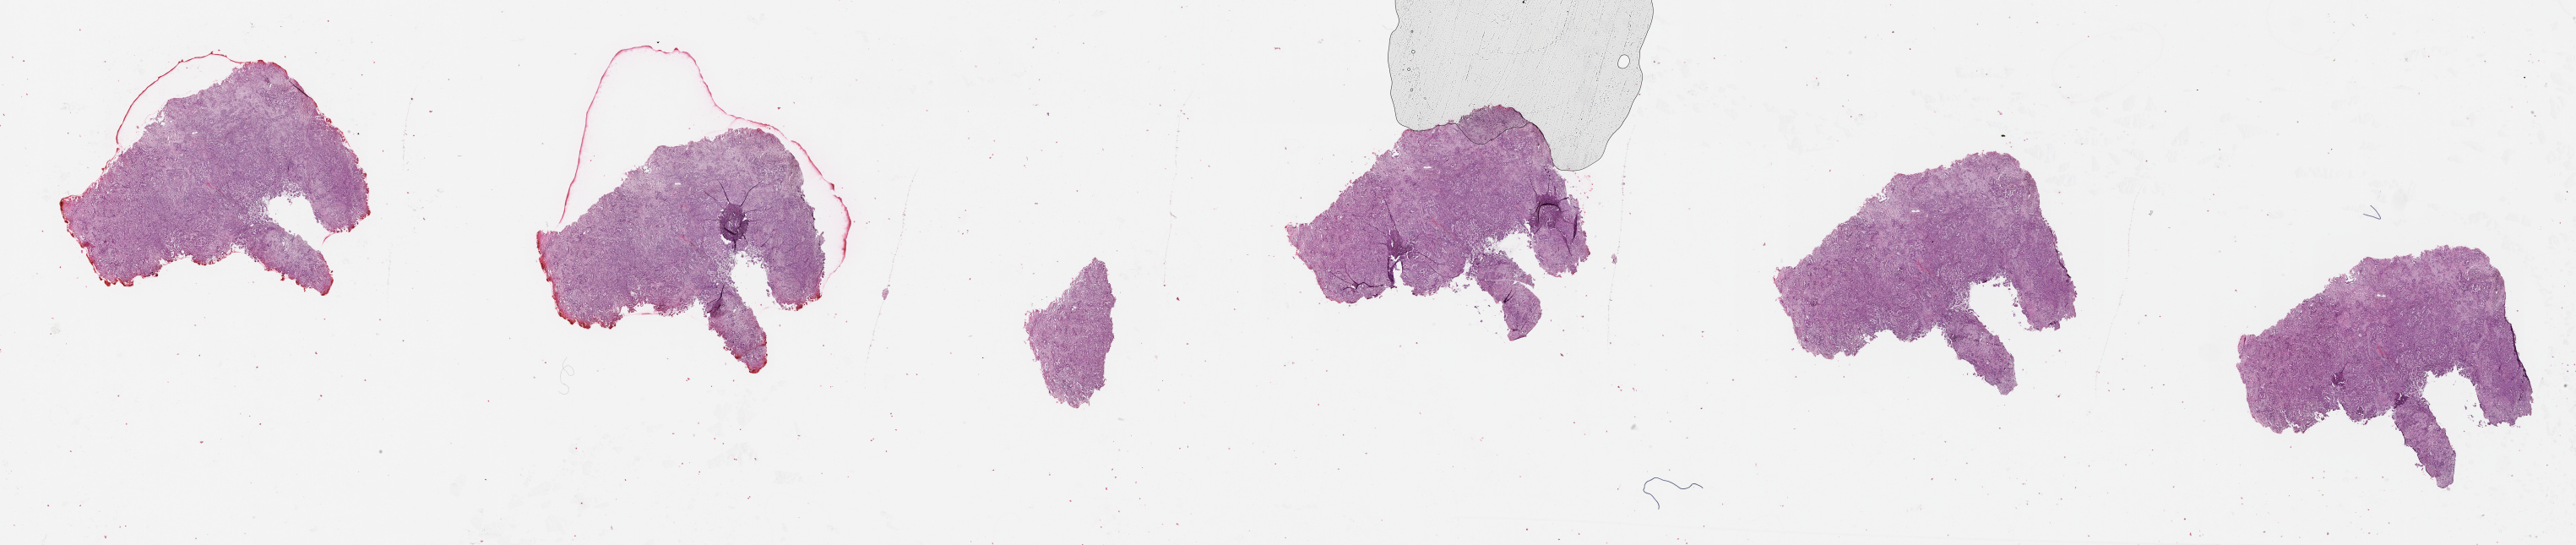
Hematoxylin and eosin (H&E) stained whole-slide image, shown as a low-resolution overview of the whole scanned area (about 49.1 x 10.4 mm, from a 20x scan); lung, tissue type not recorded.
Patient diagnosis (cohort enrolment): lung adenocarcinoma (lung).